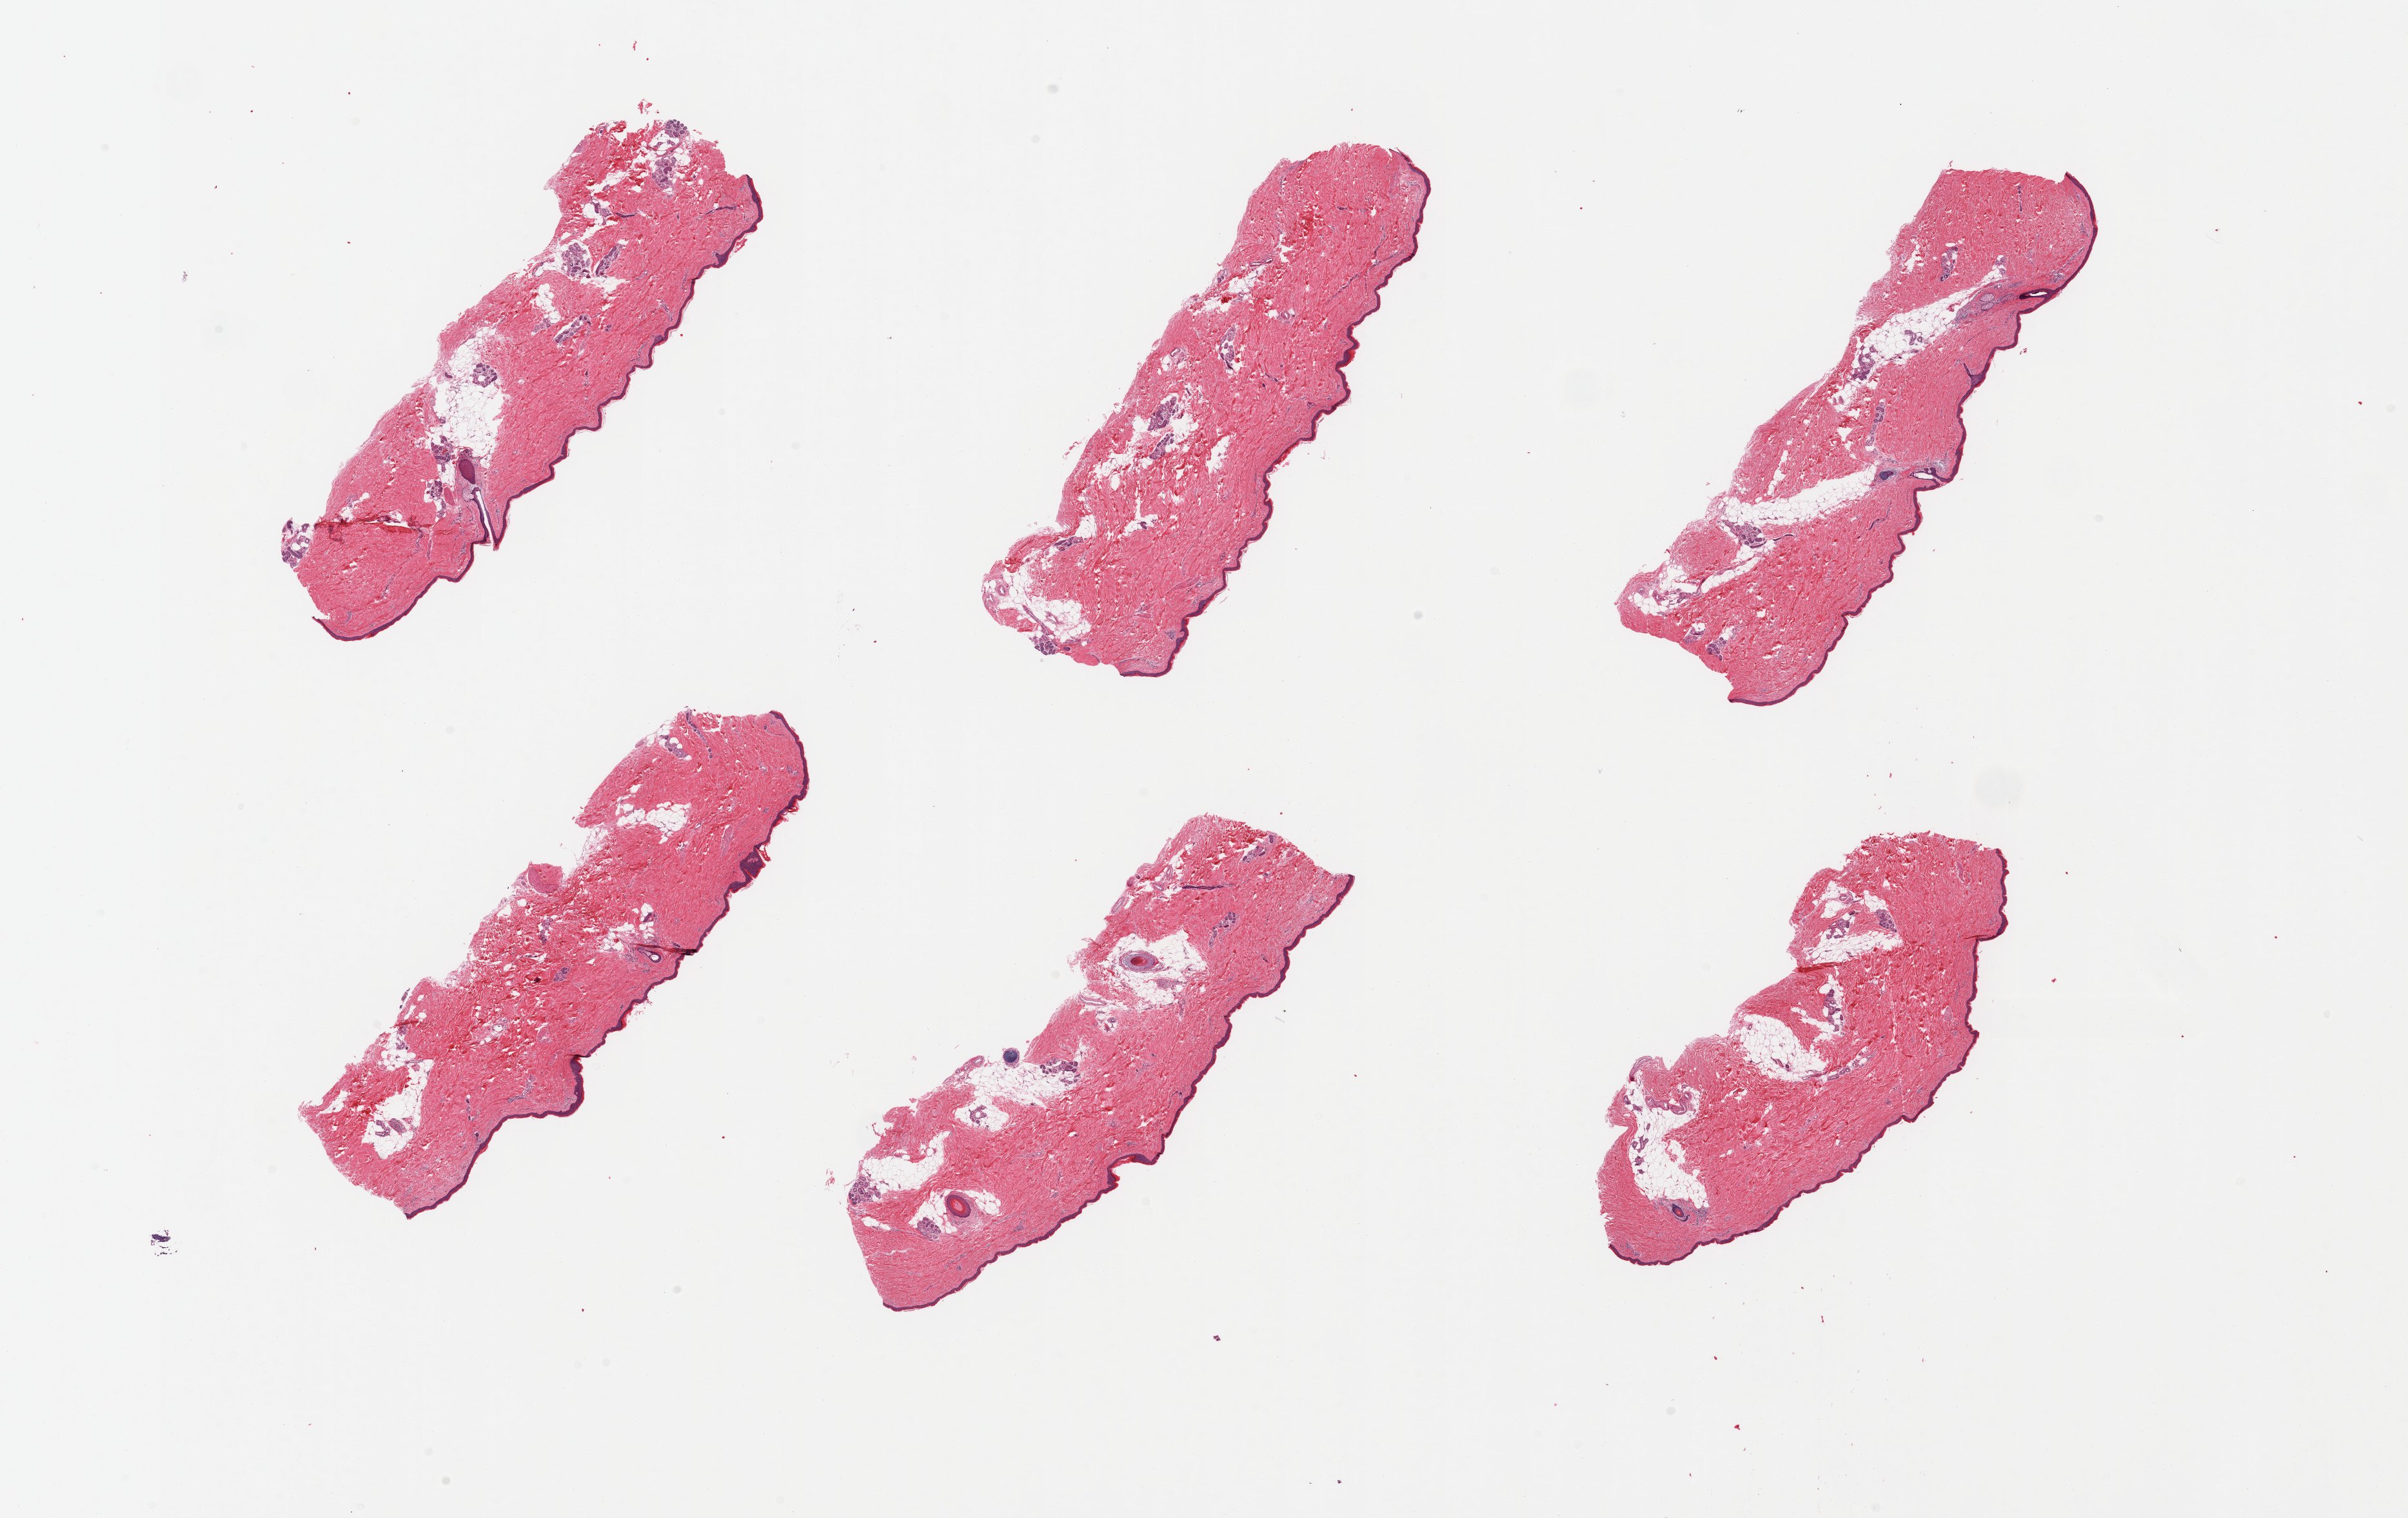
Whole-slide image, H&E stain — a low-resolution overview of the entire scanned area, about 29.5 x 18.6 mm; PAXgene-fixed, paraffin-embedded tissue; section of skin of lower leg (target tissue); tissue donor sample. Male donor.
• pathologist's review note for this sample: 6 pieces; include up to 20% mostly periadnexal fat, epidermis measures 34 microns